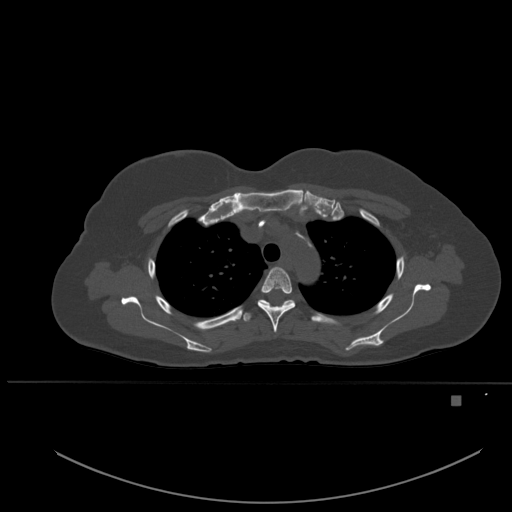
CT including the spine, one axial slice. Slice 390 of 651 in the series (ordered by position). Bone window (W 1800 / L 400 HU). 1.5 mm slice thickness. 512 × 512 image matrix, field of view 443 × 443 mm. Patient: female, 49 years. Case-level facts recorded for this patient, not image findings: primary cancer: breast.
Structures marked on this image (semi-automatic segmentation, software-assisted and operator-edited):
- T3 vertebra: bounding box <258,267,295,333> (left, top, right, bottom; pixels)
- T4 vertebra: <239,299,295,322>